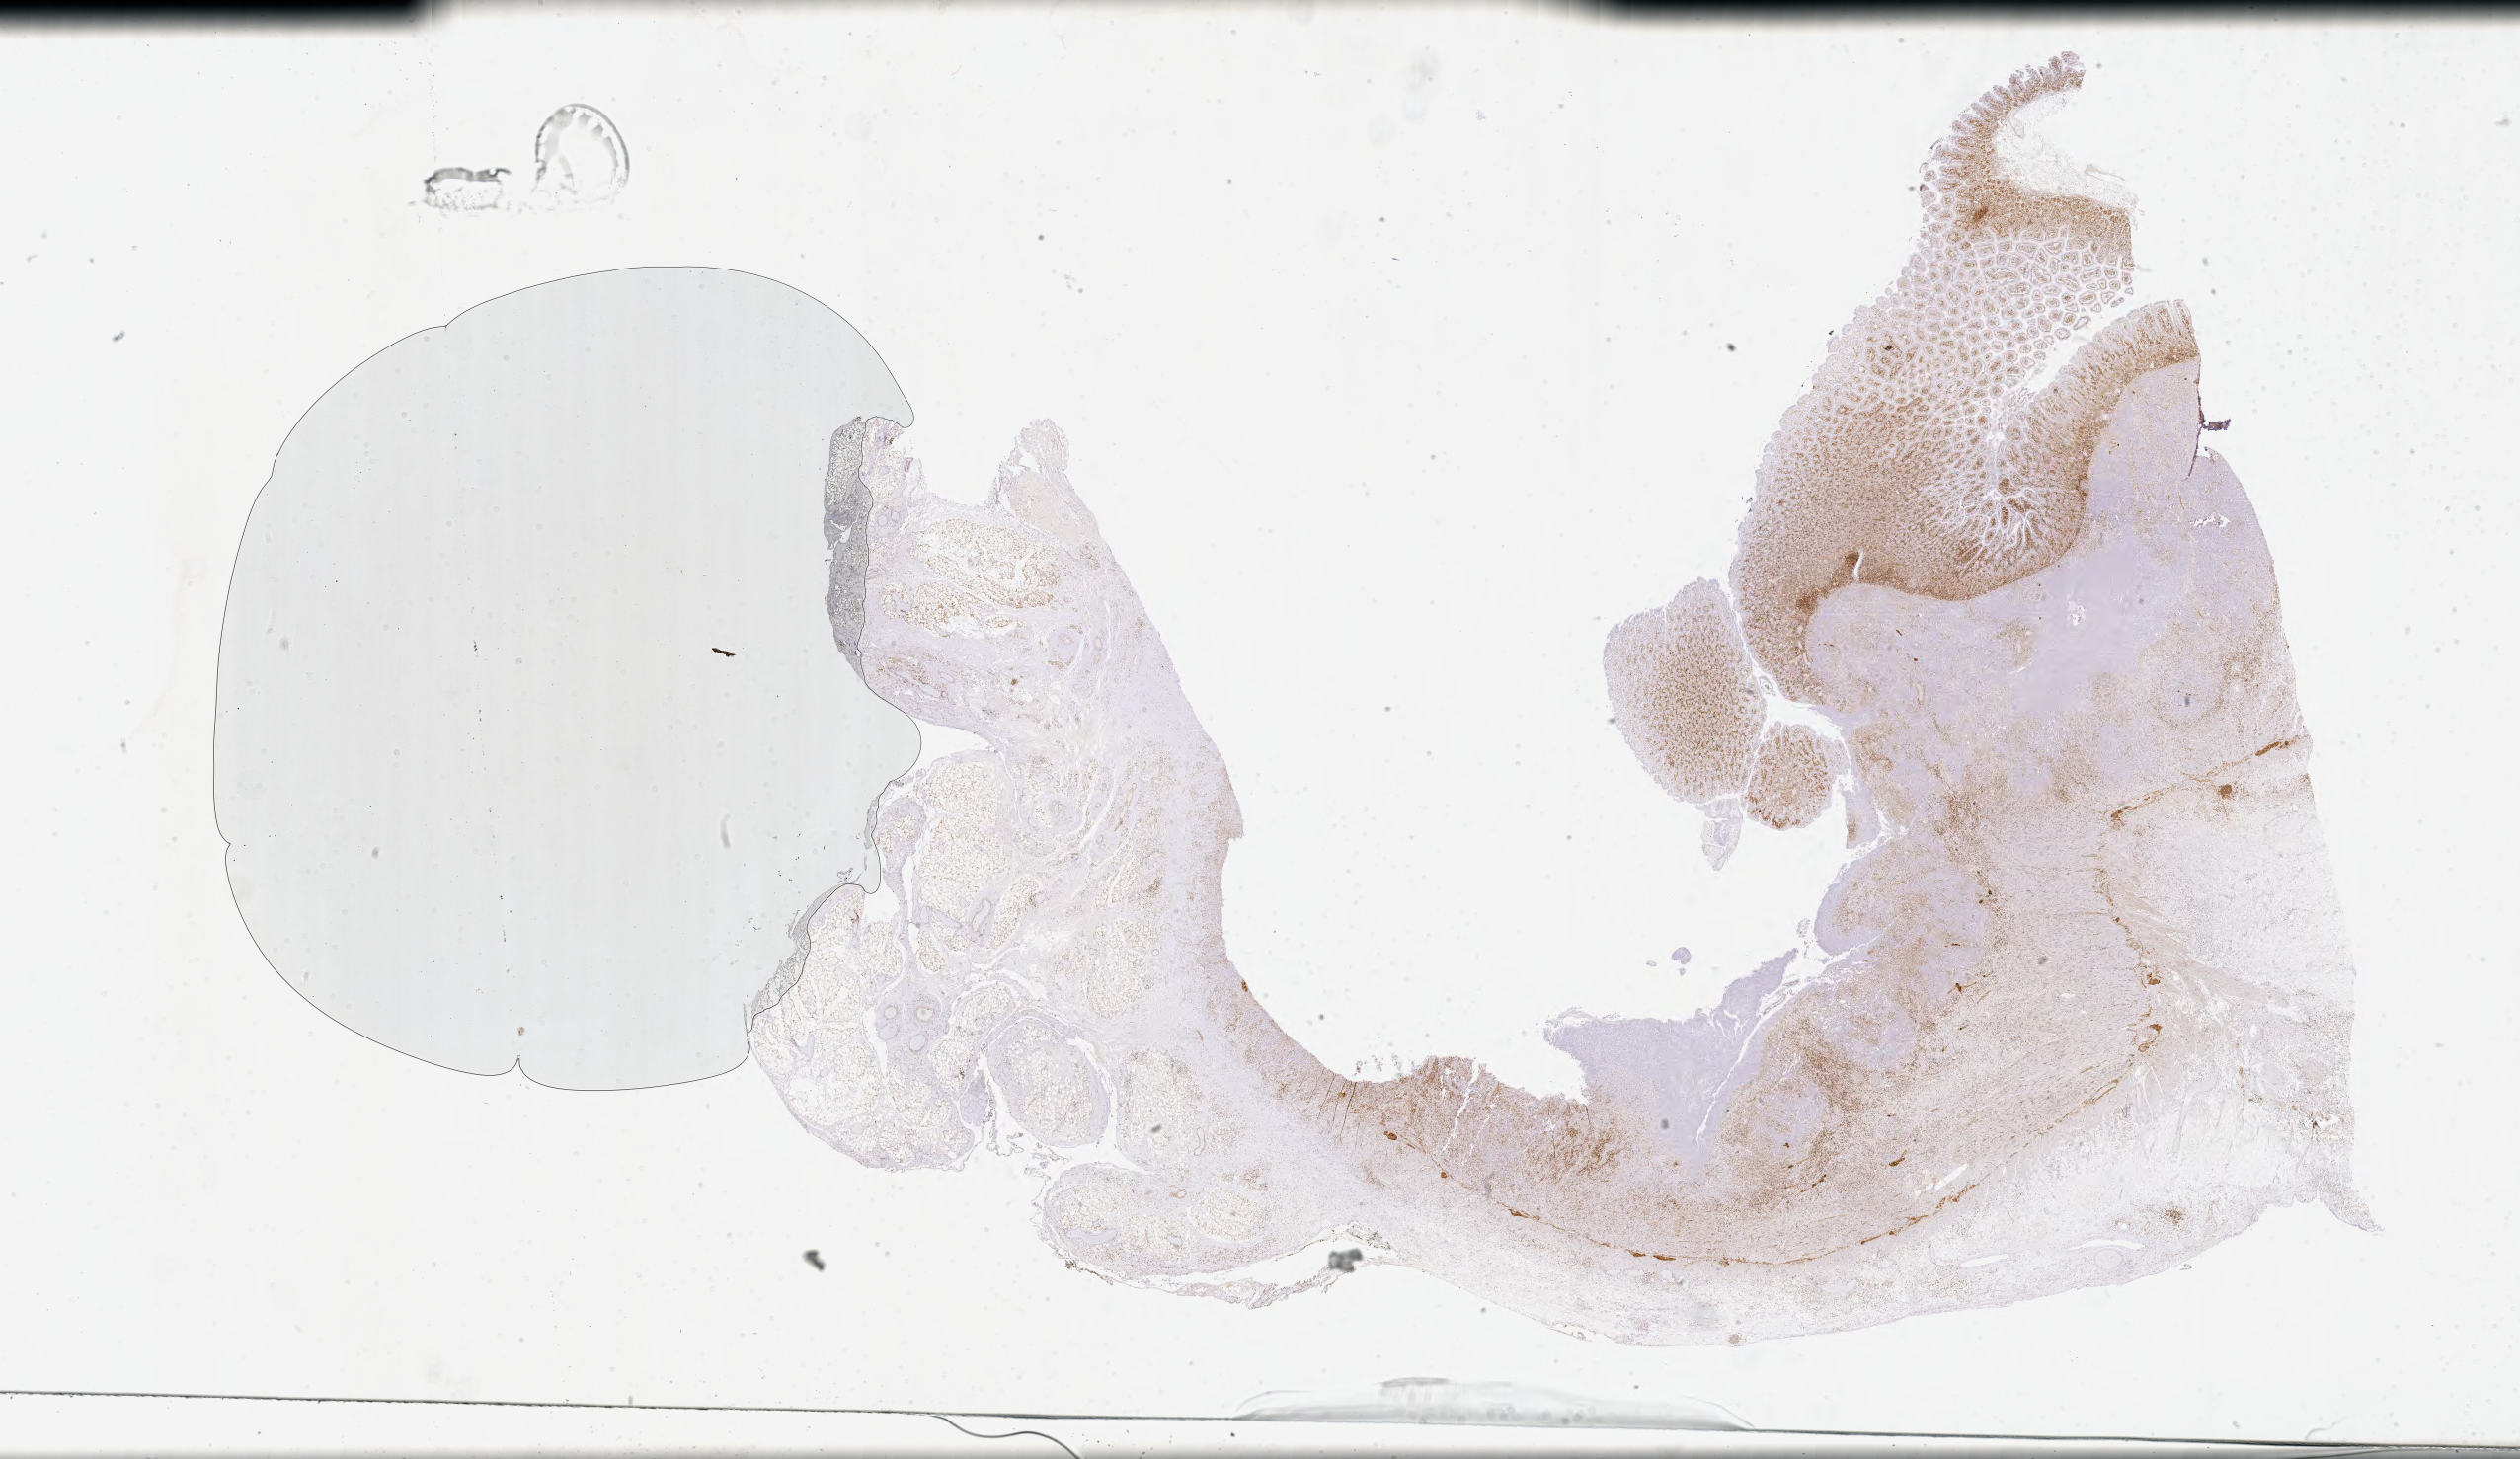
Immunohistochemistry (IHC) whole-slide image stained for BCL2 — low-resolution overview of the scanned area, about 41.2 x 23.9 mm, specimen: tumor tissue. Patient: female, 44 years old.
• diagnosis: Burkitt lymphoma, NOS